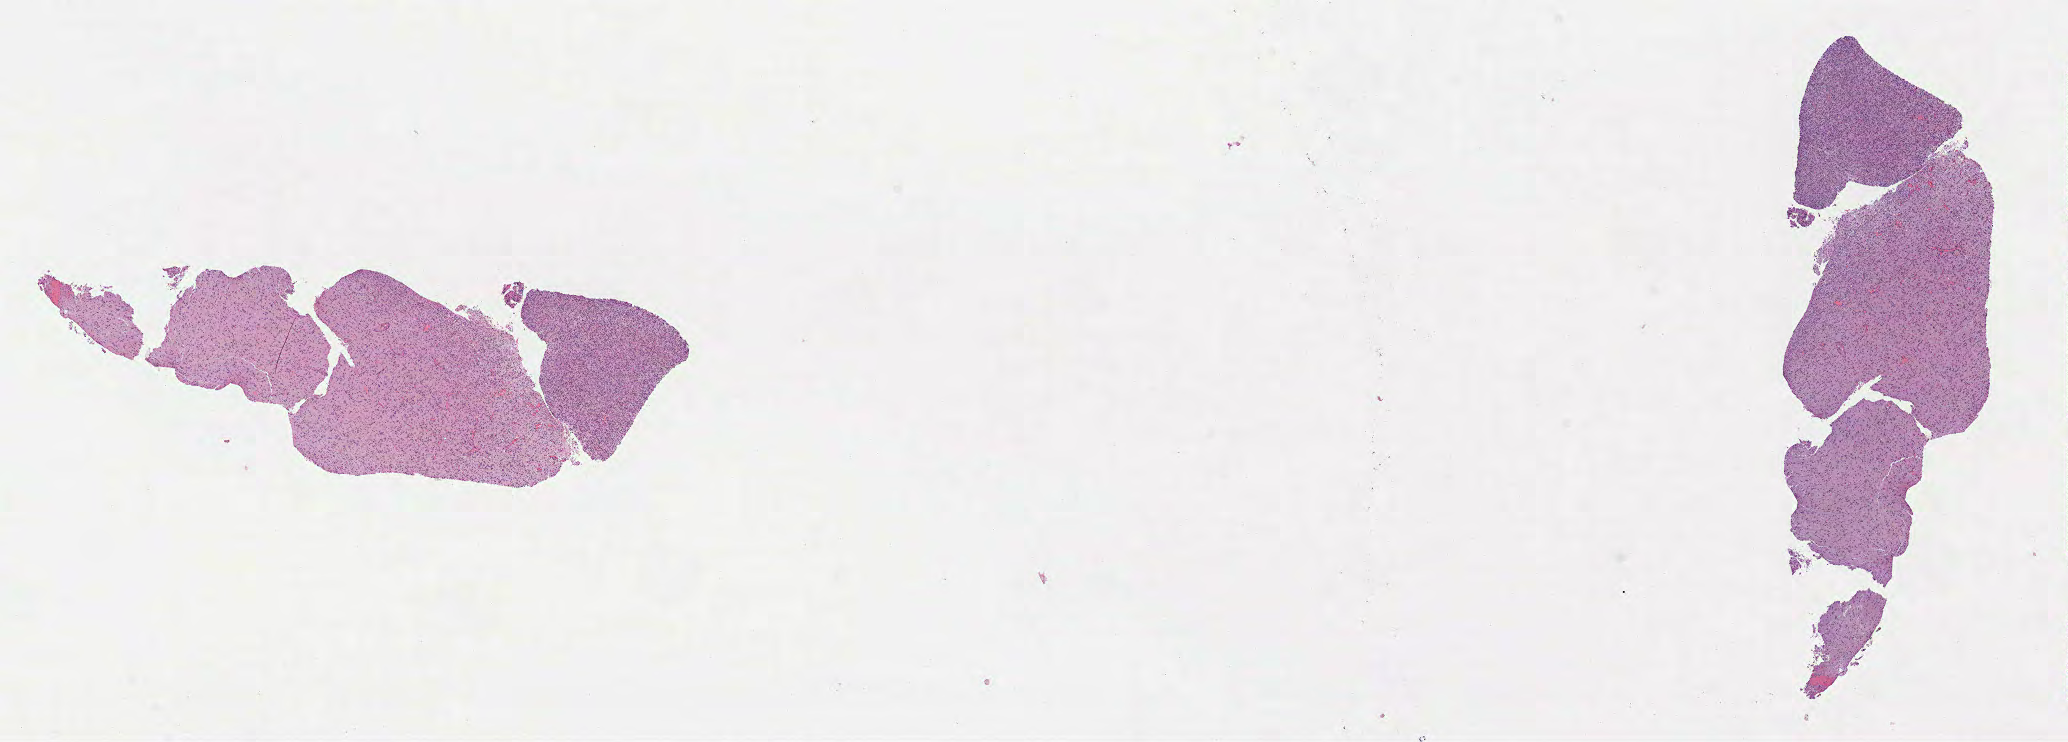
Whole-slide histology image, Hematoxylin and eosin (H&E) stained, low-resolution overview of the scanned area, about 16.7 x 6.0 mm; FFPE section; sample: primary tumour, brain. Patient: female, age at initial diagnosis 50 years.
Pathologic diagnosis: Glioblastoma.